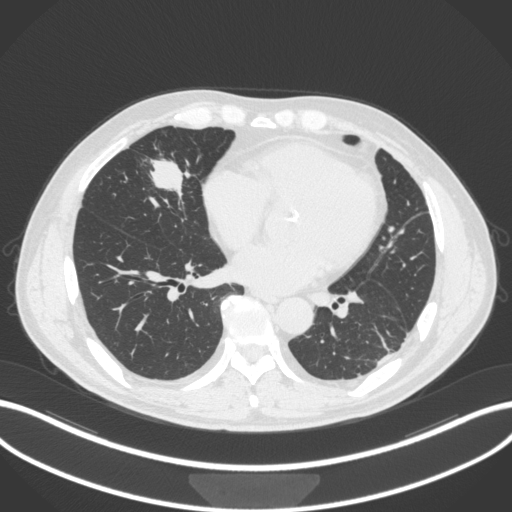
Chest CT, one axial slice. Slice 111 of 399 in the series (ordered by position). Reconstruction kernel B31f. 120 kVp. Lung window (W 1500 / L -600 HU). 512 × 512 image matrix, field of view 400 × 400 mm. Patient: male, 59 years. From the clinical record (not read from this slice): clinical TNM (as recorded): T2a N1 M0.
Annotated regions visible in this slice (bounding box drawn by a radiologist):
- lung tumour (recorded histology: adenocarcinoma): bounding box [x1, y1, x2, y2] px = [140, 150, 195, 202]